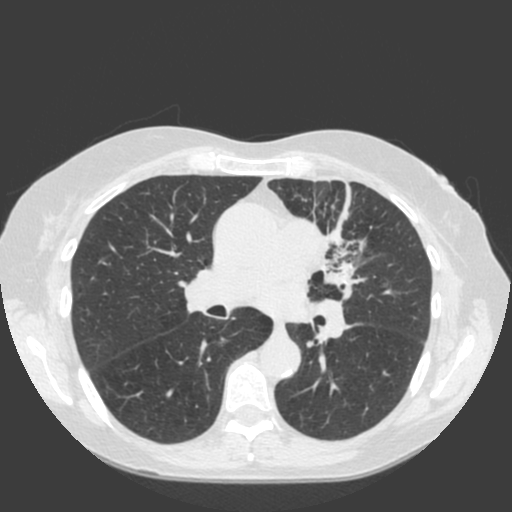
Low-dose screening chest CT, axial slice, first (baseline) screen, lung window (W 1500 / L -600 HU), standard (soft-tissue) reconstruction kernel (C), 120 kVp, slice 76 of 184 in the series. Female, age 66 years at enrolment. Current smoker at enrolment.
Expert reader's lesion annotation, bounding box <276,198,403,313> (left, top, right, bottom; pixels). Reader record for this screening exam (exam-level; its link to the box is not recorded): non-calcified nodule or mass ≥4 mm, left upper lobe, 61 × 45 mm, spiculated (stellate) margins, soft tissue attenuation. Official screen result: positive, change unspecified: nodule(s) >= 4 mm or enlarging nodule(s), mass(es), or other non-specific abnormalities suspicious for lung cancer.